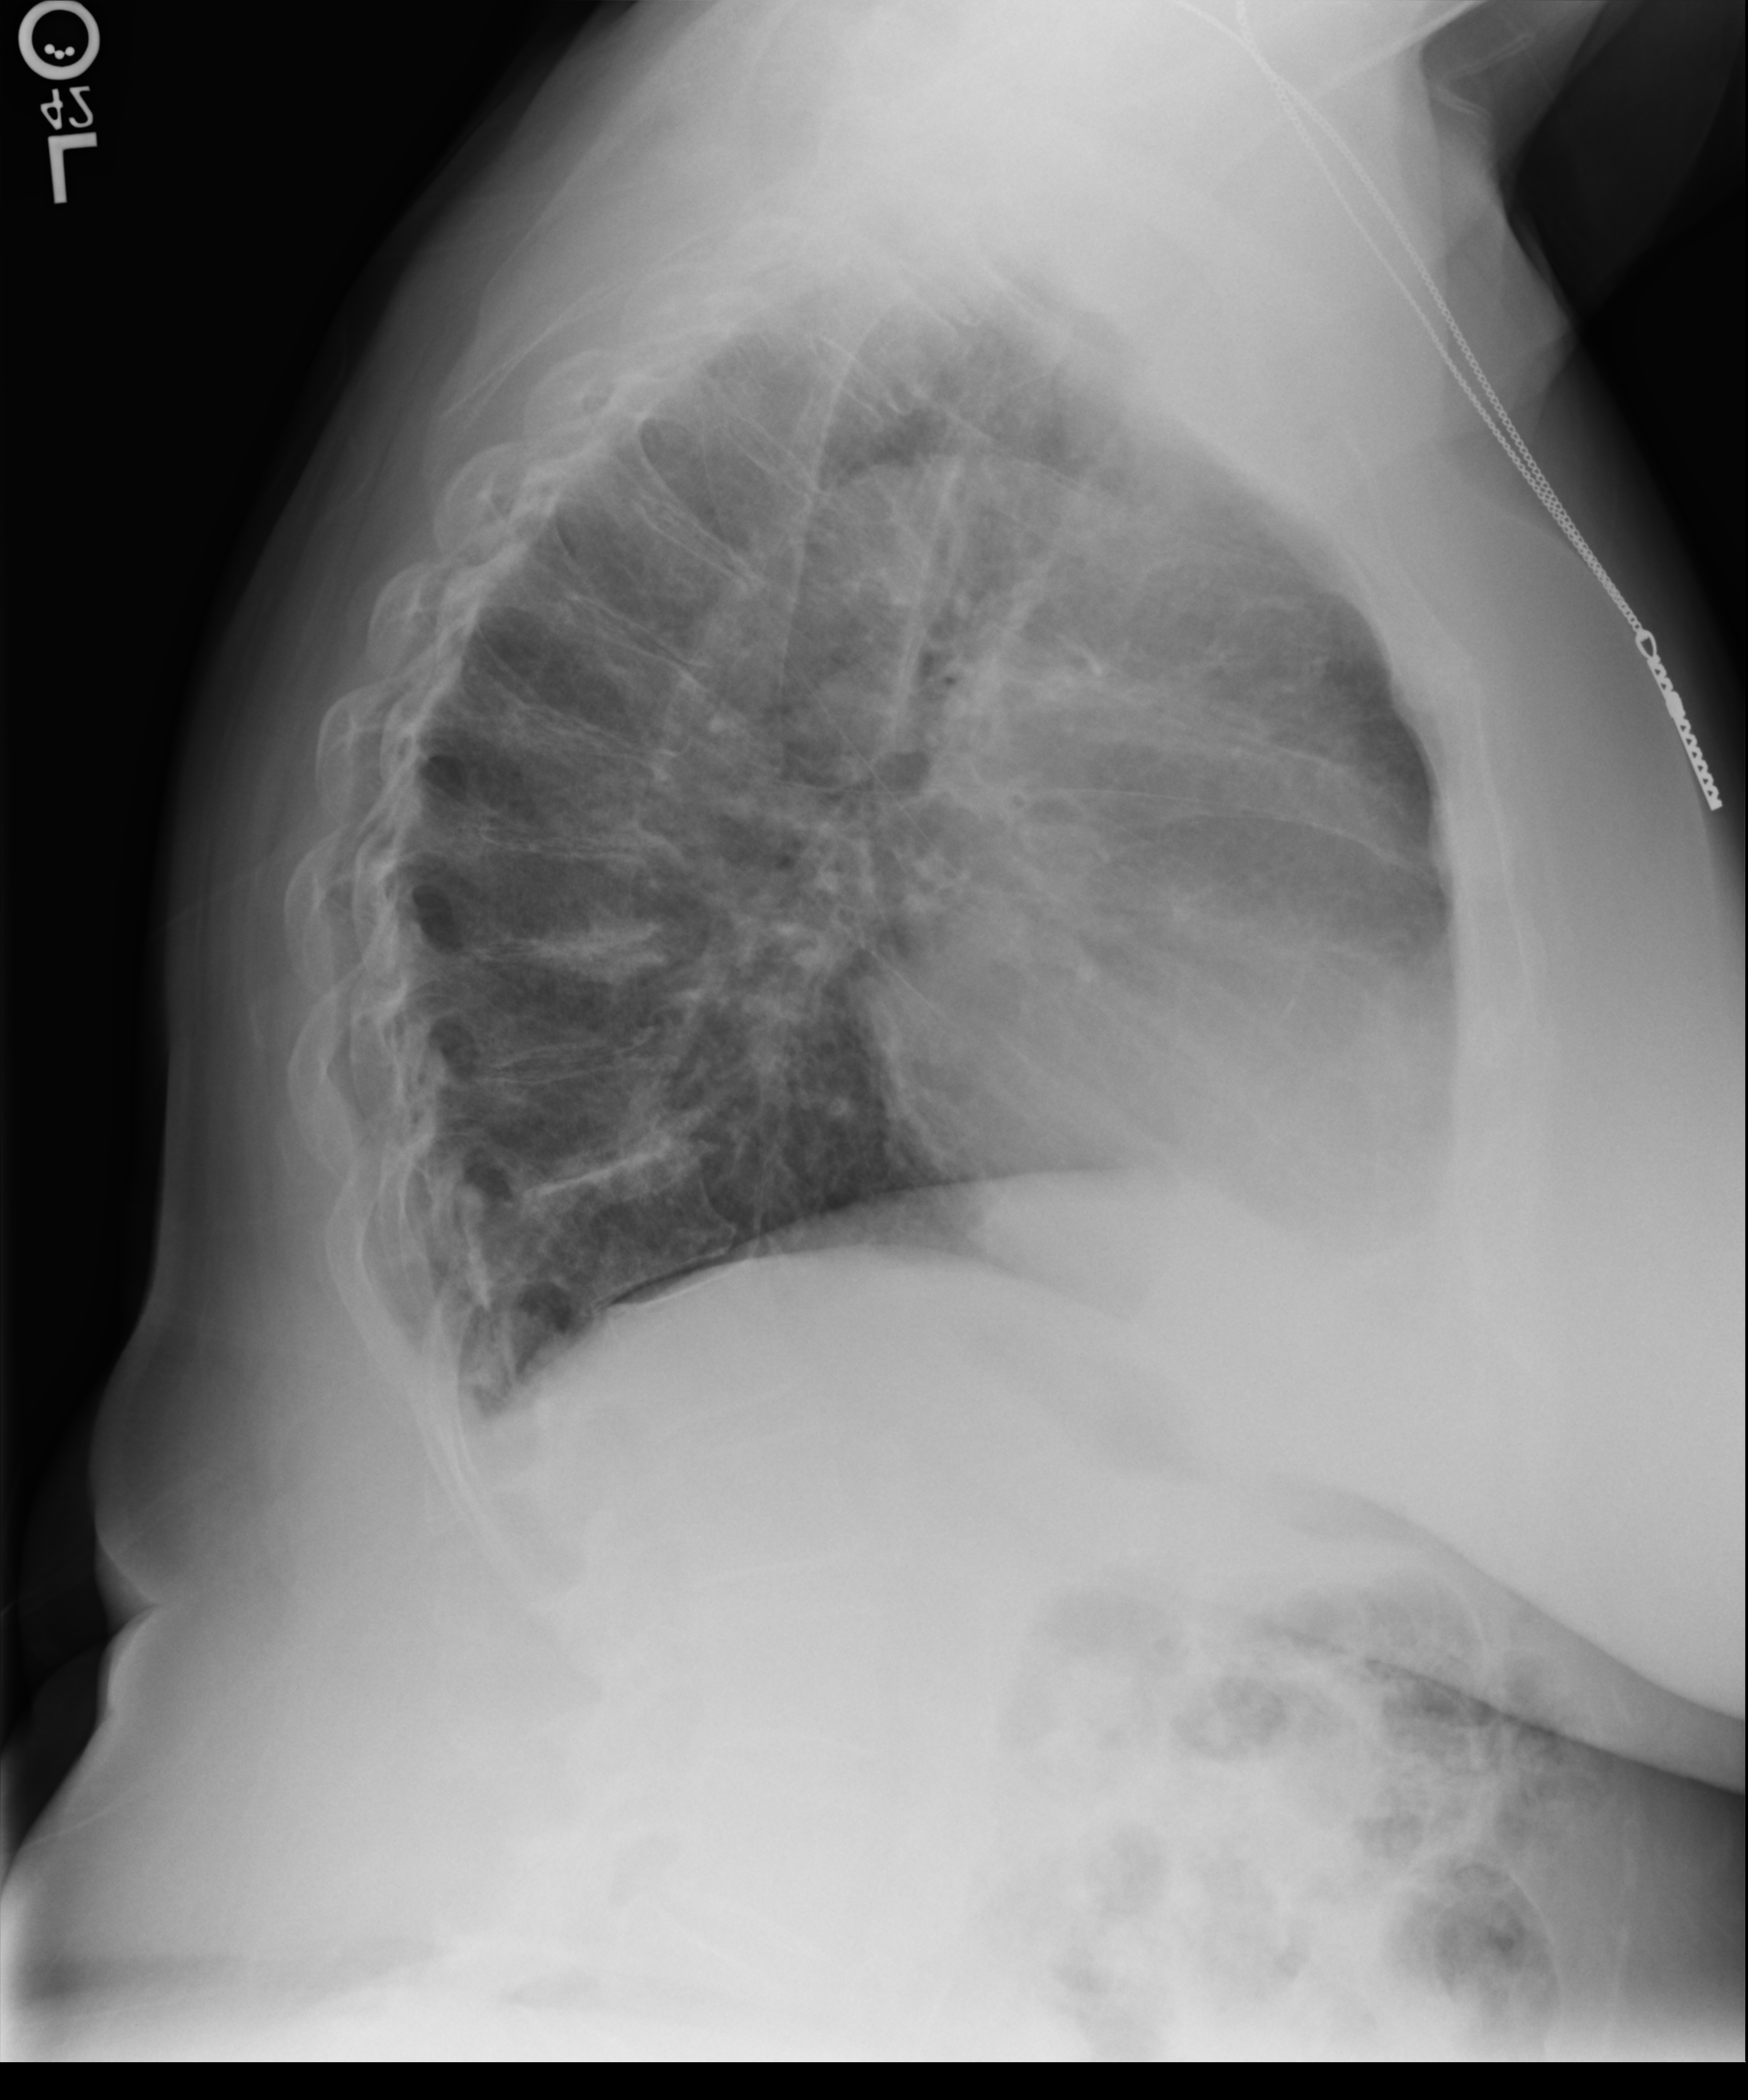
Chest radiograph, lateral projection. Female patient hospitalised with COVID-19, age 75–90 years.
Hospital-stay facts (about this admission, not read from this image; timing relative to this image not recorded): mechanically ventilated during this hospital stay: no.